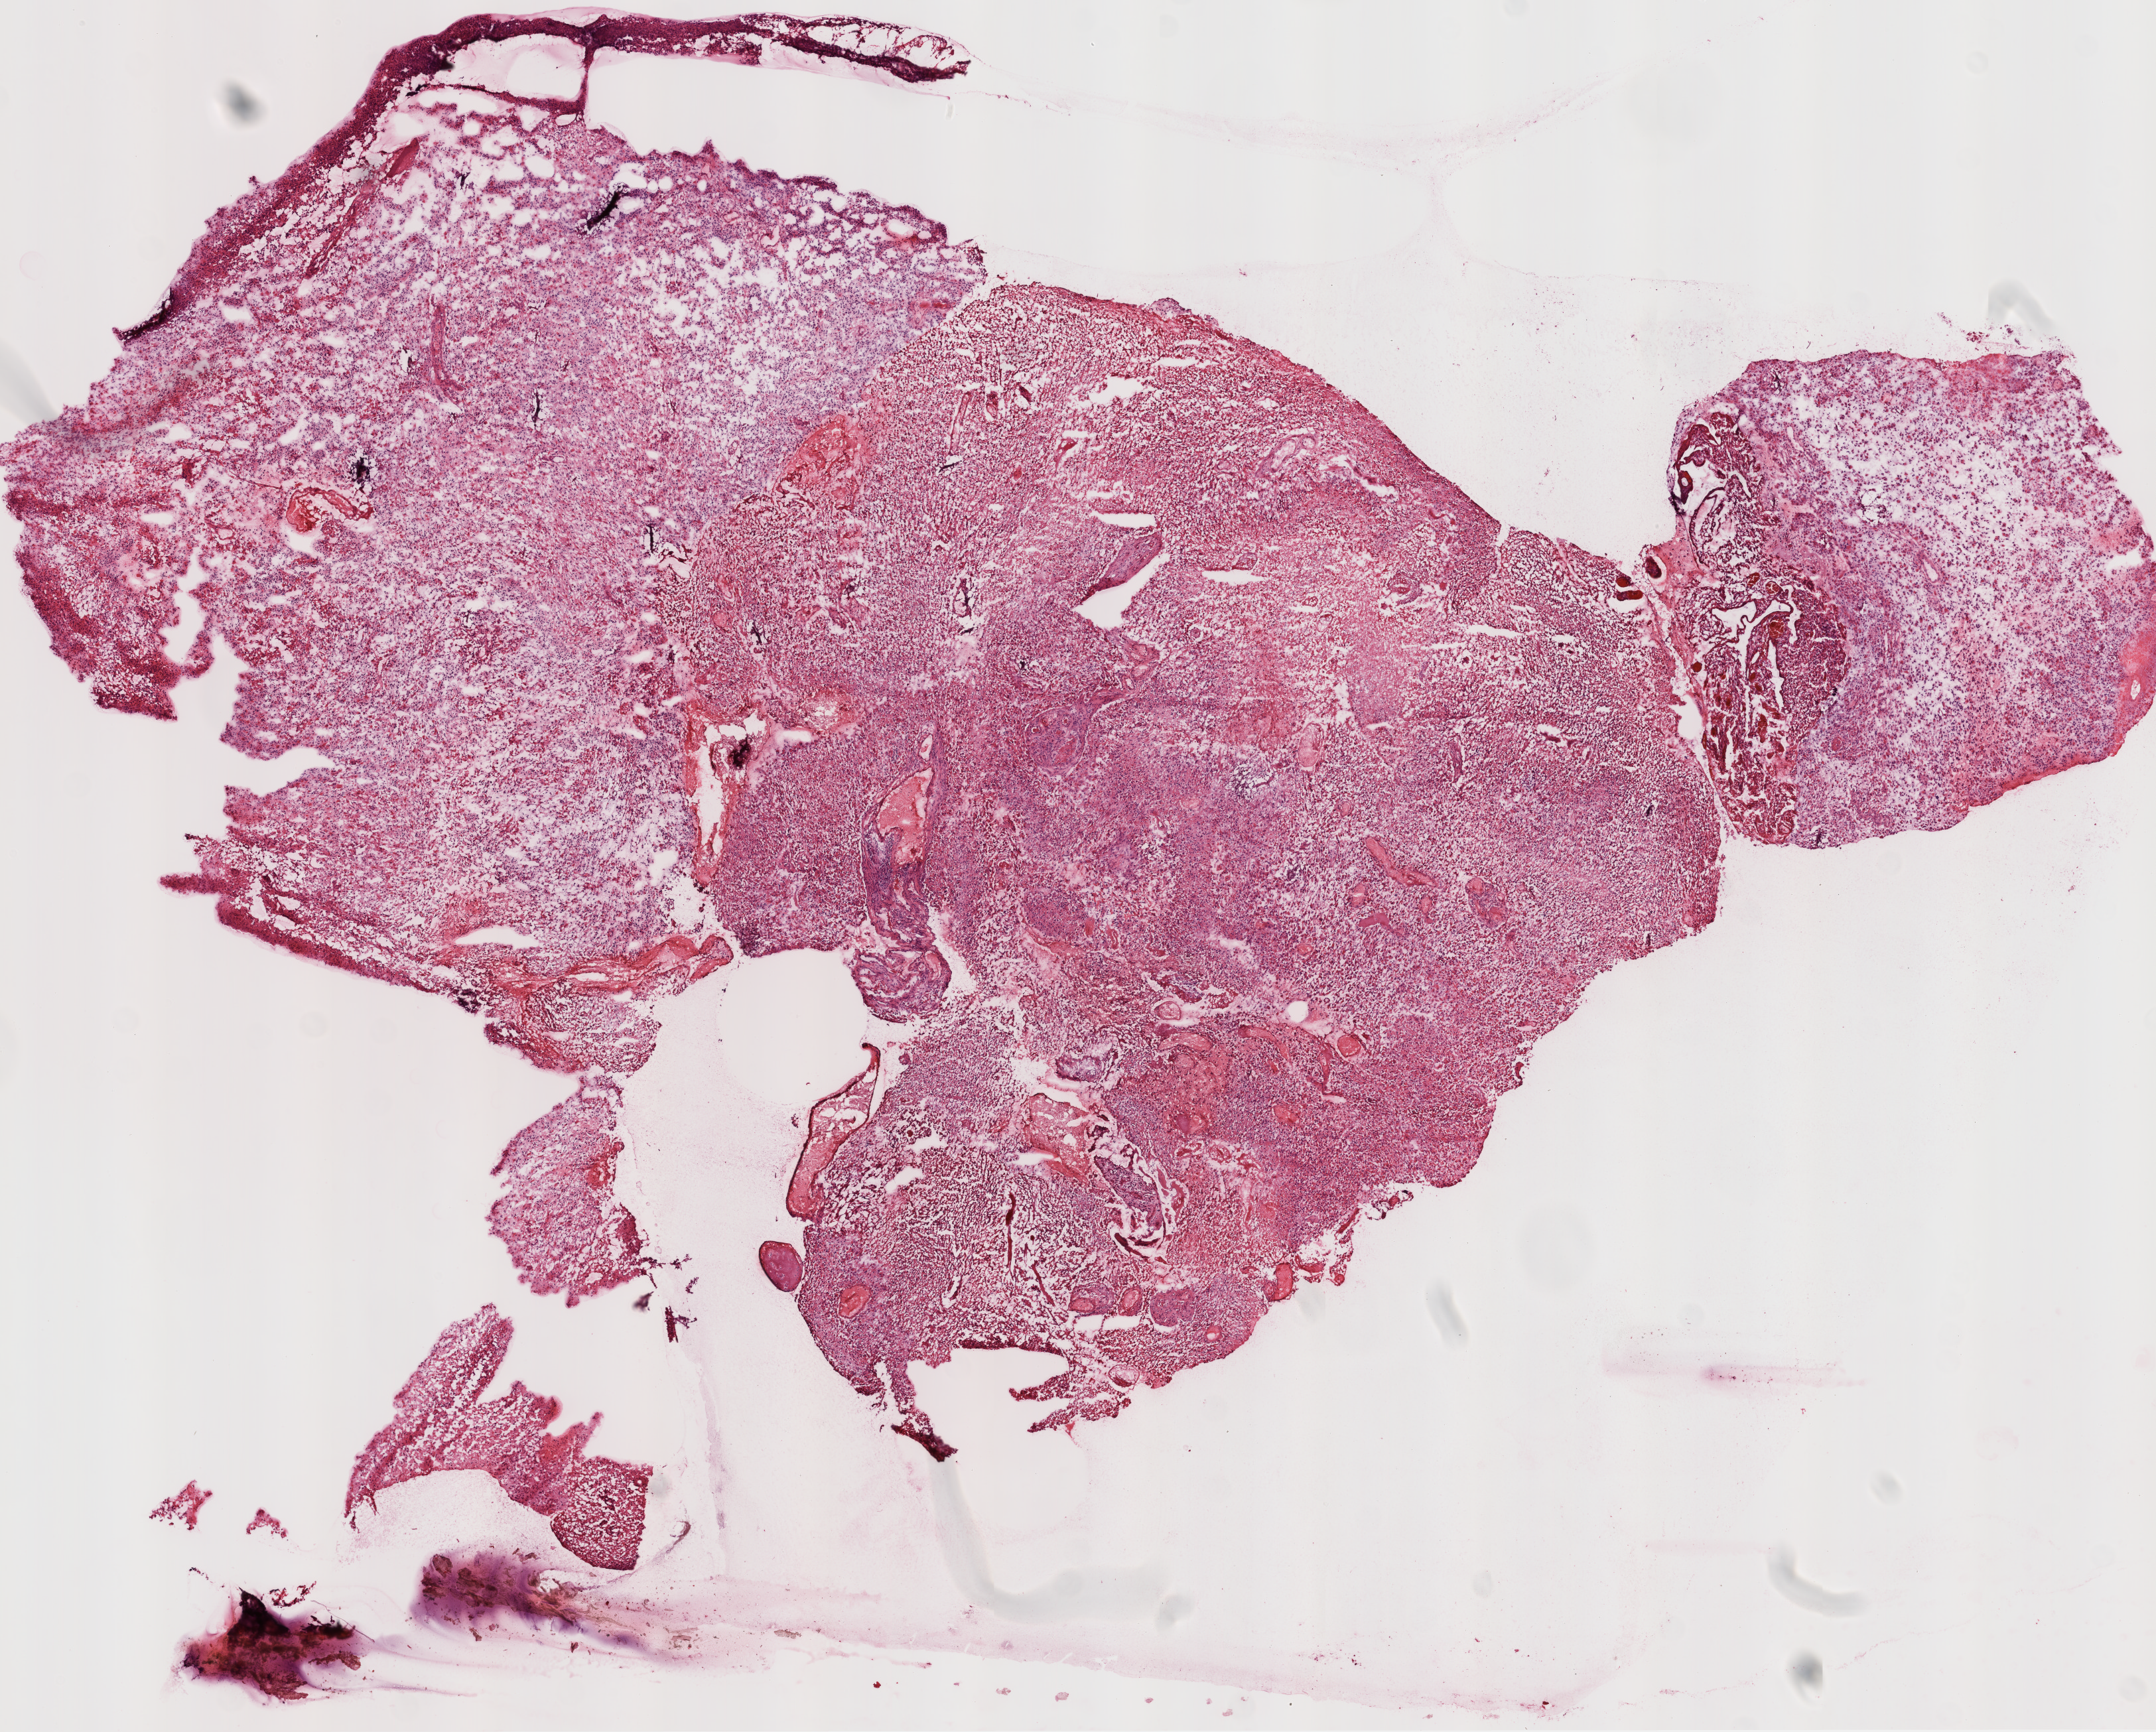
H&E whole-slide image, whole scanned area (about 13.0 x 10.5 mm) shown as a low-resolution overview, frozen section from the top of the tissue portion, brain, primary tumour sample. Patient: male, age at initial diagnosis 58 years. Slide review estimates, as recorded: tumour cells 60%, tumour nuclei 80%, normal cells 0%, stromal cells 10%, necrosis 30%.
* histologic diagnosis: Glioblastoma